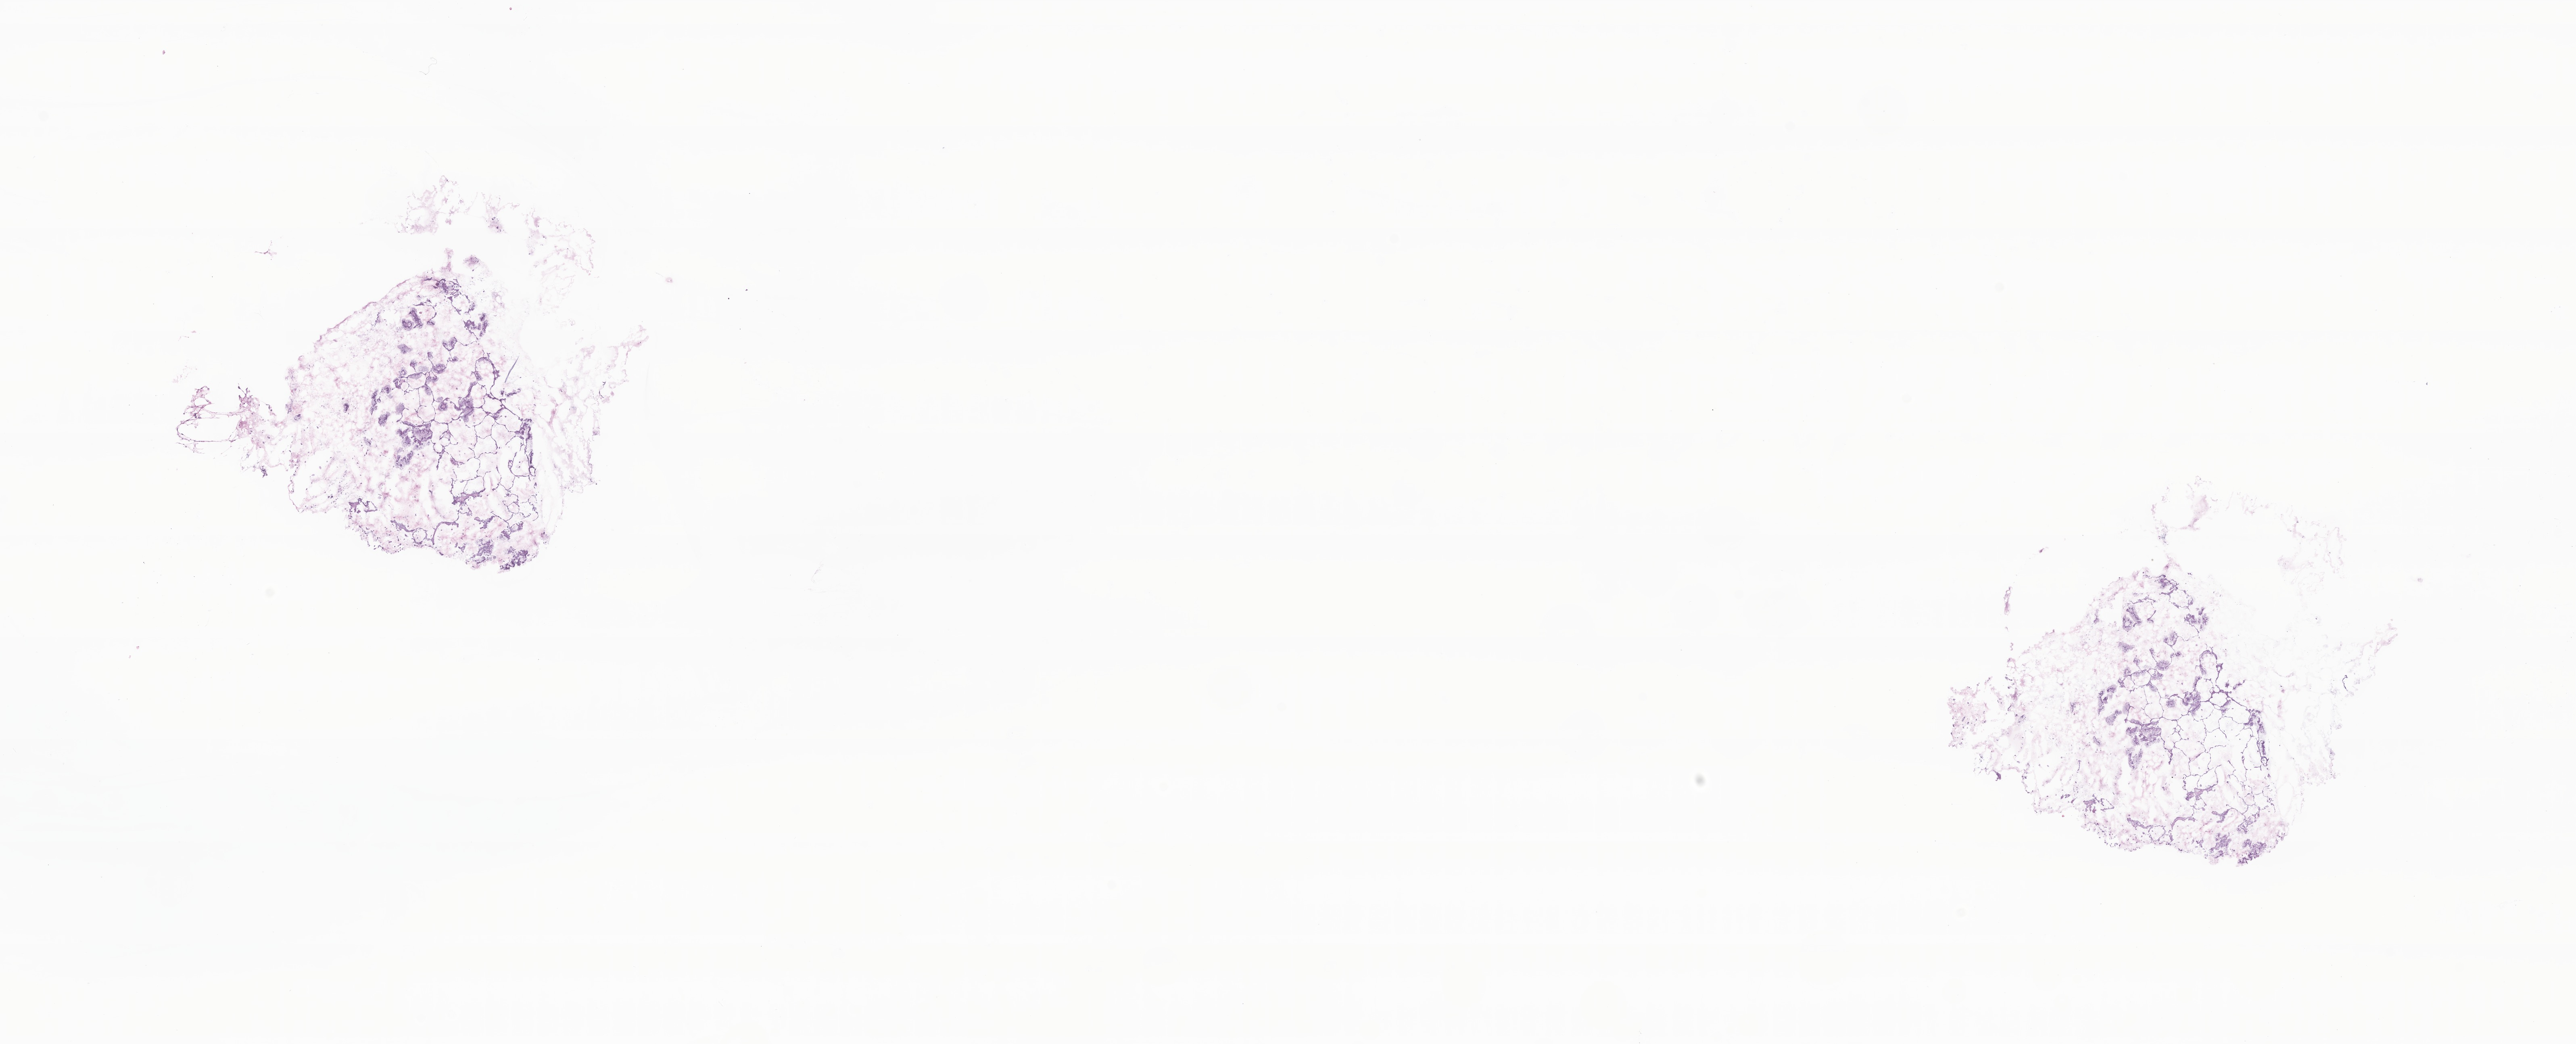
Hematoxylin and eosin (H&E) whole-slide image — shown as a low-resolution overview of the whole scanned area (about 26.9 x 10.9 mm), frozen section, primary tumor, site: upper lobe of left lung. Female, age 52 years at initial diagnosis. Pathologist review of this section (percent, as recorded): tumor cells 50%, tumor nuclei 45%, stromal cells 0%, necrosis 0%, normal cells 50%. Inflammatory infiltration, as recorded: lymphocyte infiltration 0%, monocyte infiltration 0%, neutrophil infiltration 0%.
* section: top of the tissue portion
* diagnosis: Adenocarcinoma of lung, mucinous